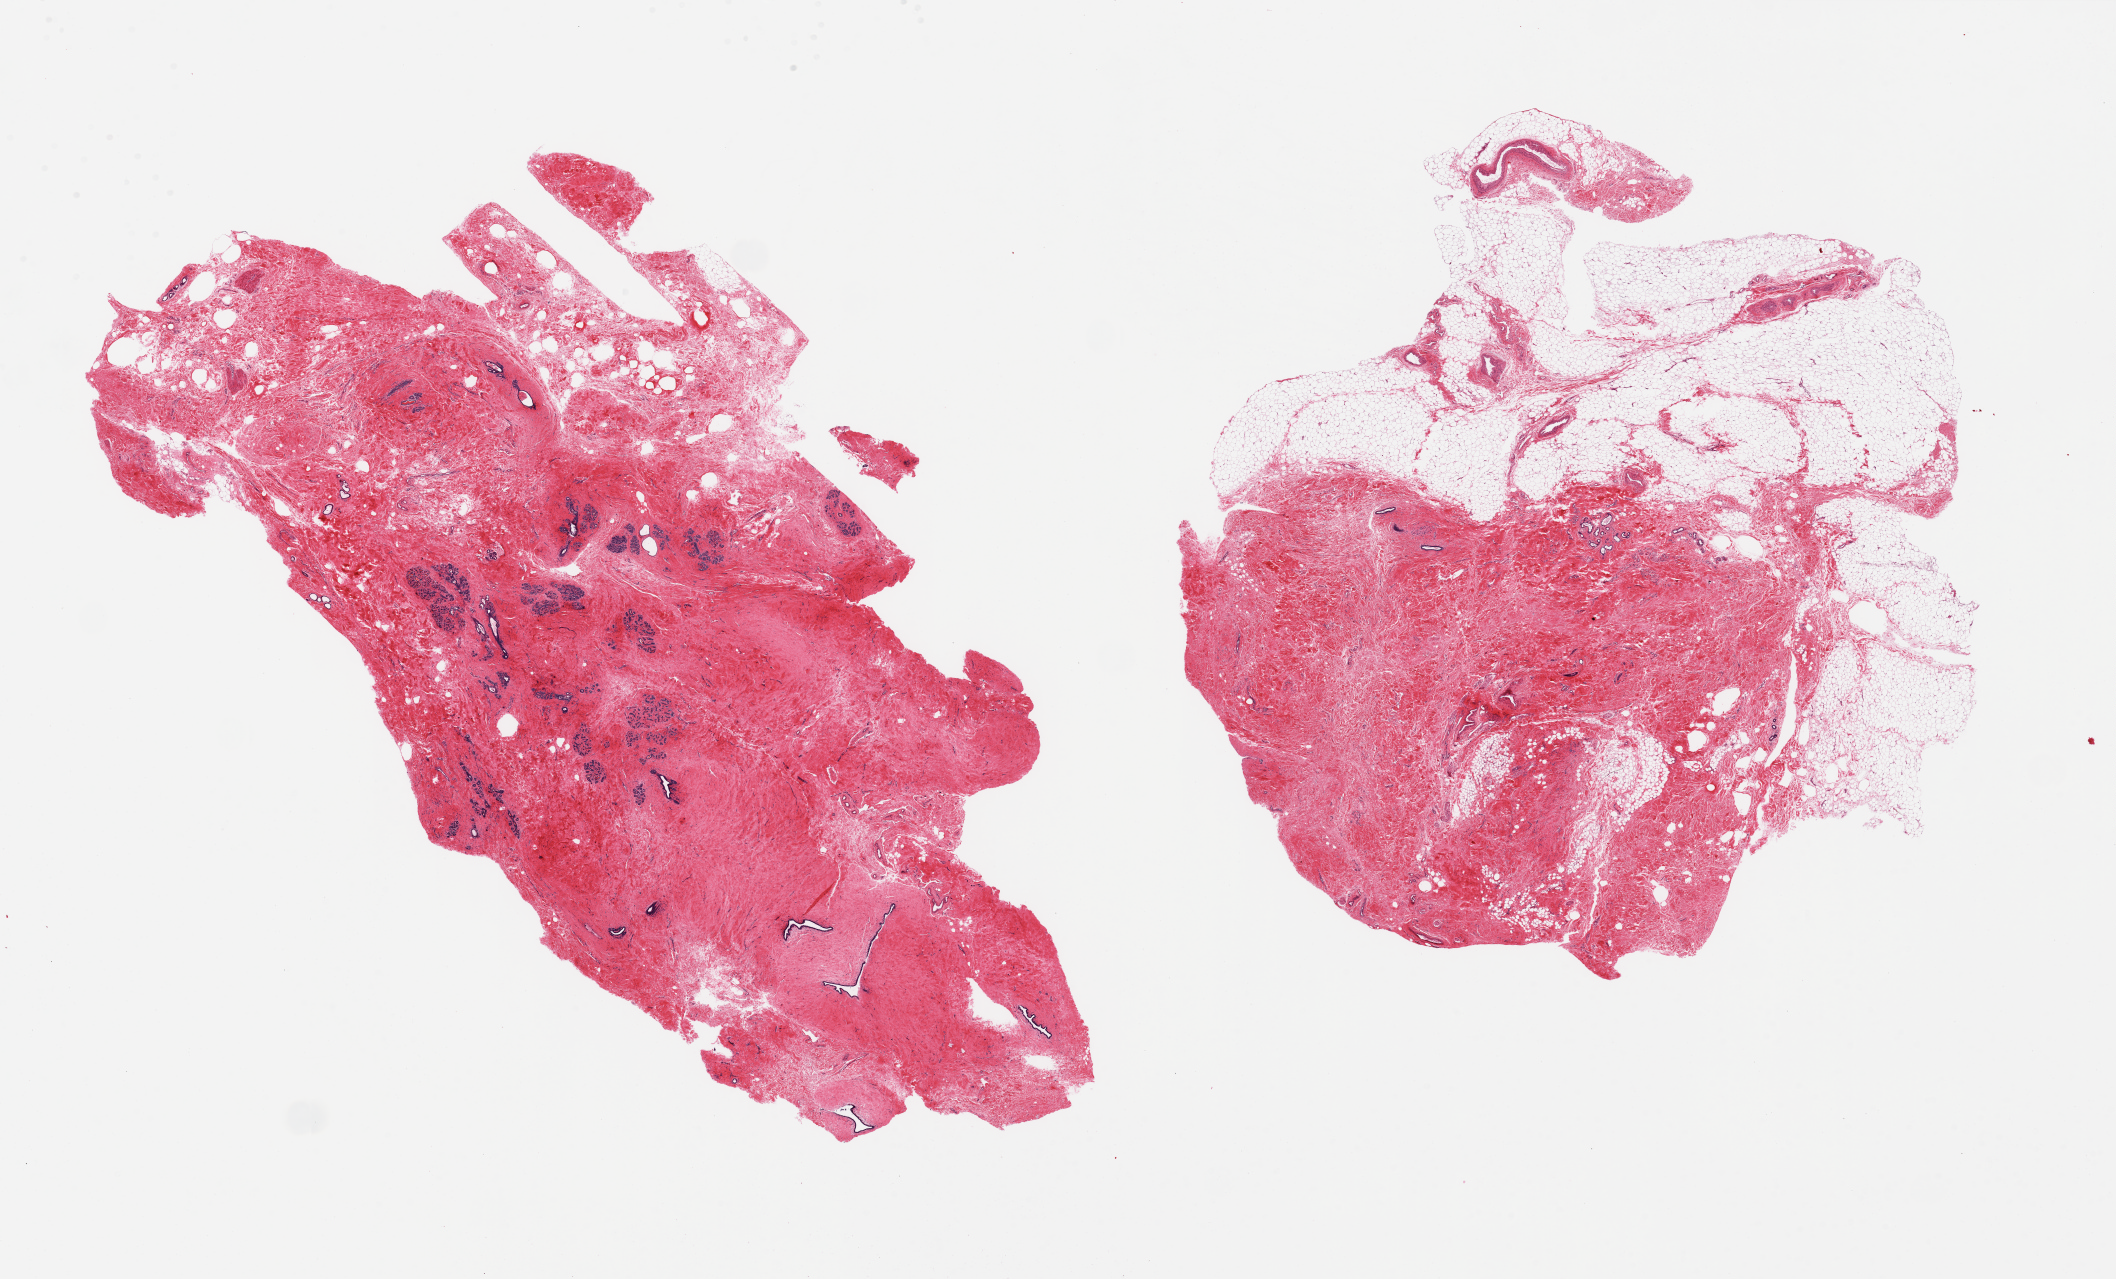
Digitized hematoxylin and eosin (H&E)-stained section — low-resolution overview of the scanned area, about 33.5 x 20.2 mm (slide scanned at 20x); PAXgene-fixed, paraffin-embedded tissue; sampled site (target tissue): breast; tissue donor sample.
Reviewer comment on this tissue sample: 2 pieces, well preserved but inactive appearing TDLUs in one section.